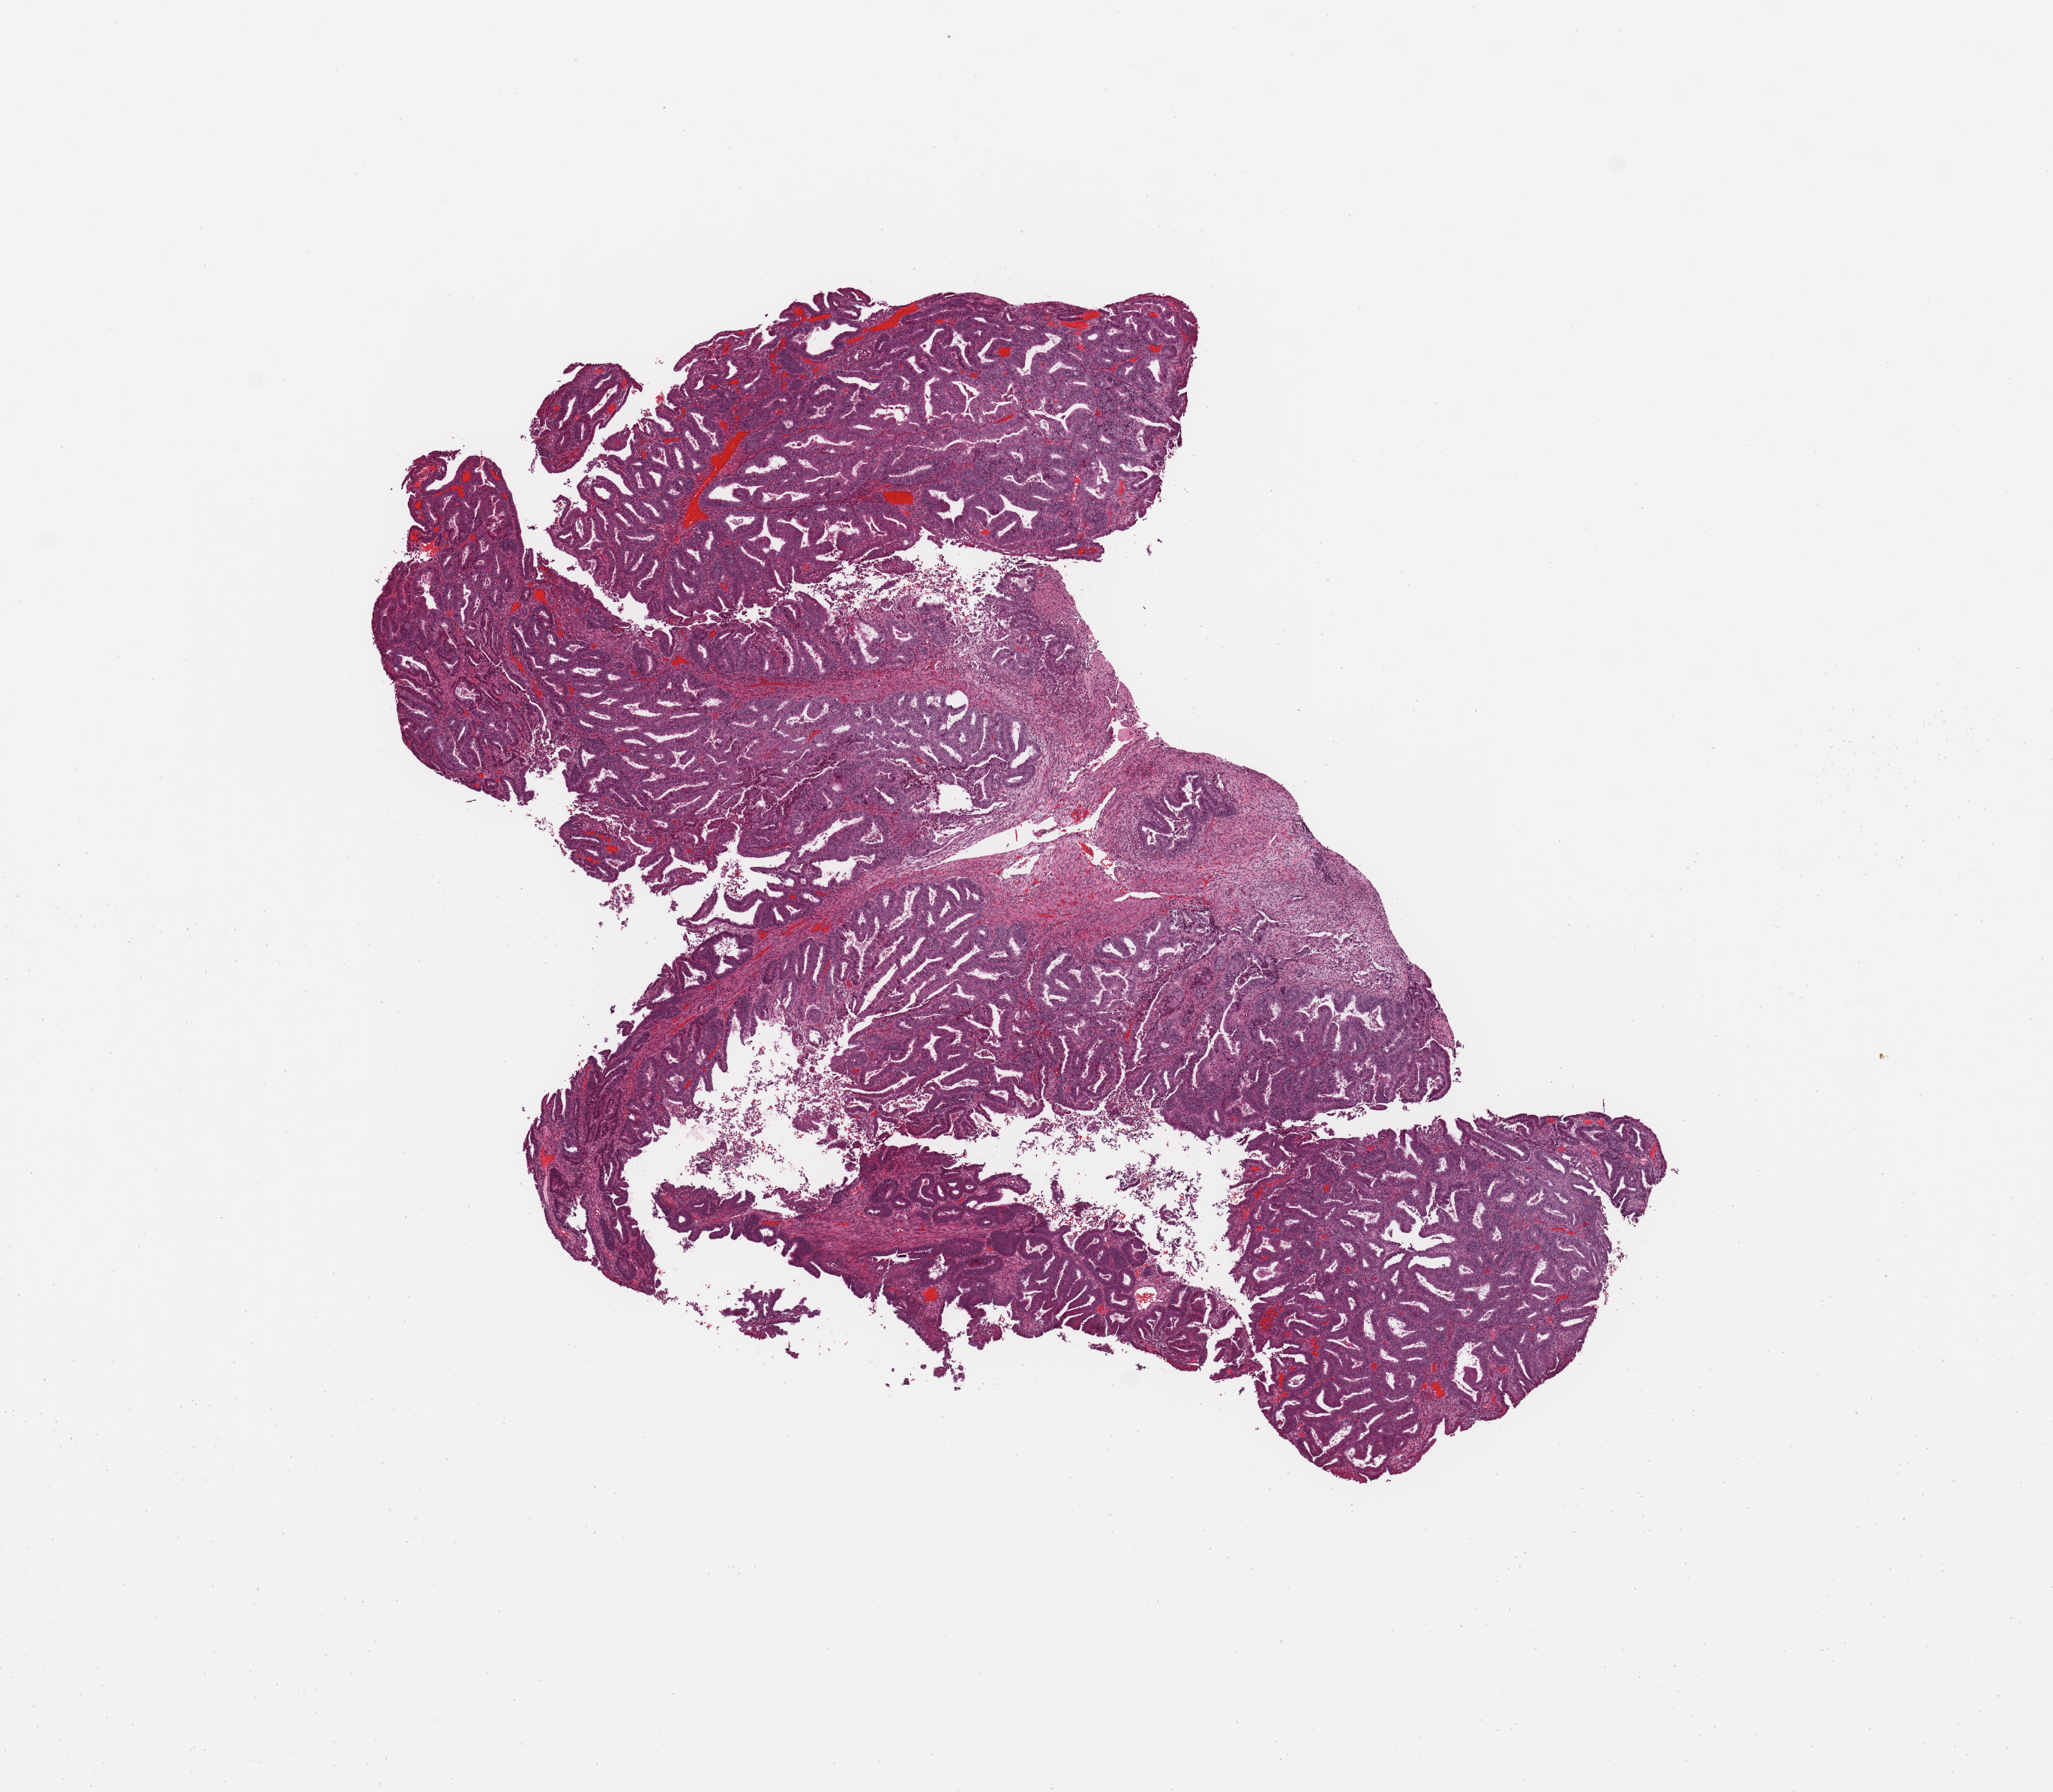
Whole-slide histology image, Hematoxylin and eosin (H&E) stained, a low-resolution overview of the entire scanned area, about 10.8 x 9.5 mm, tumour tissue sample, sampled site: uterus. Female, 56 y/o. Histologic grade: G1 (well differentiated). Slide review estimates, as recorded: tumour nuclei 90%, necrosis 0%.
AJCC pathologic stage: I. Diagnosis: Endometrioid adenocarcinoma, NOS.